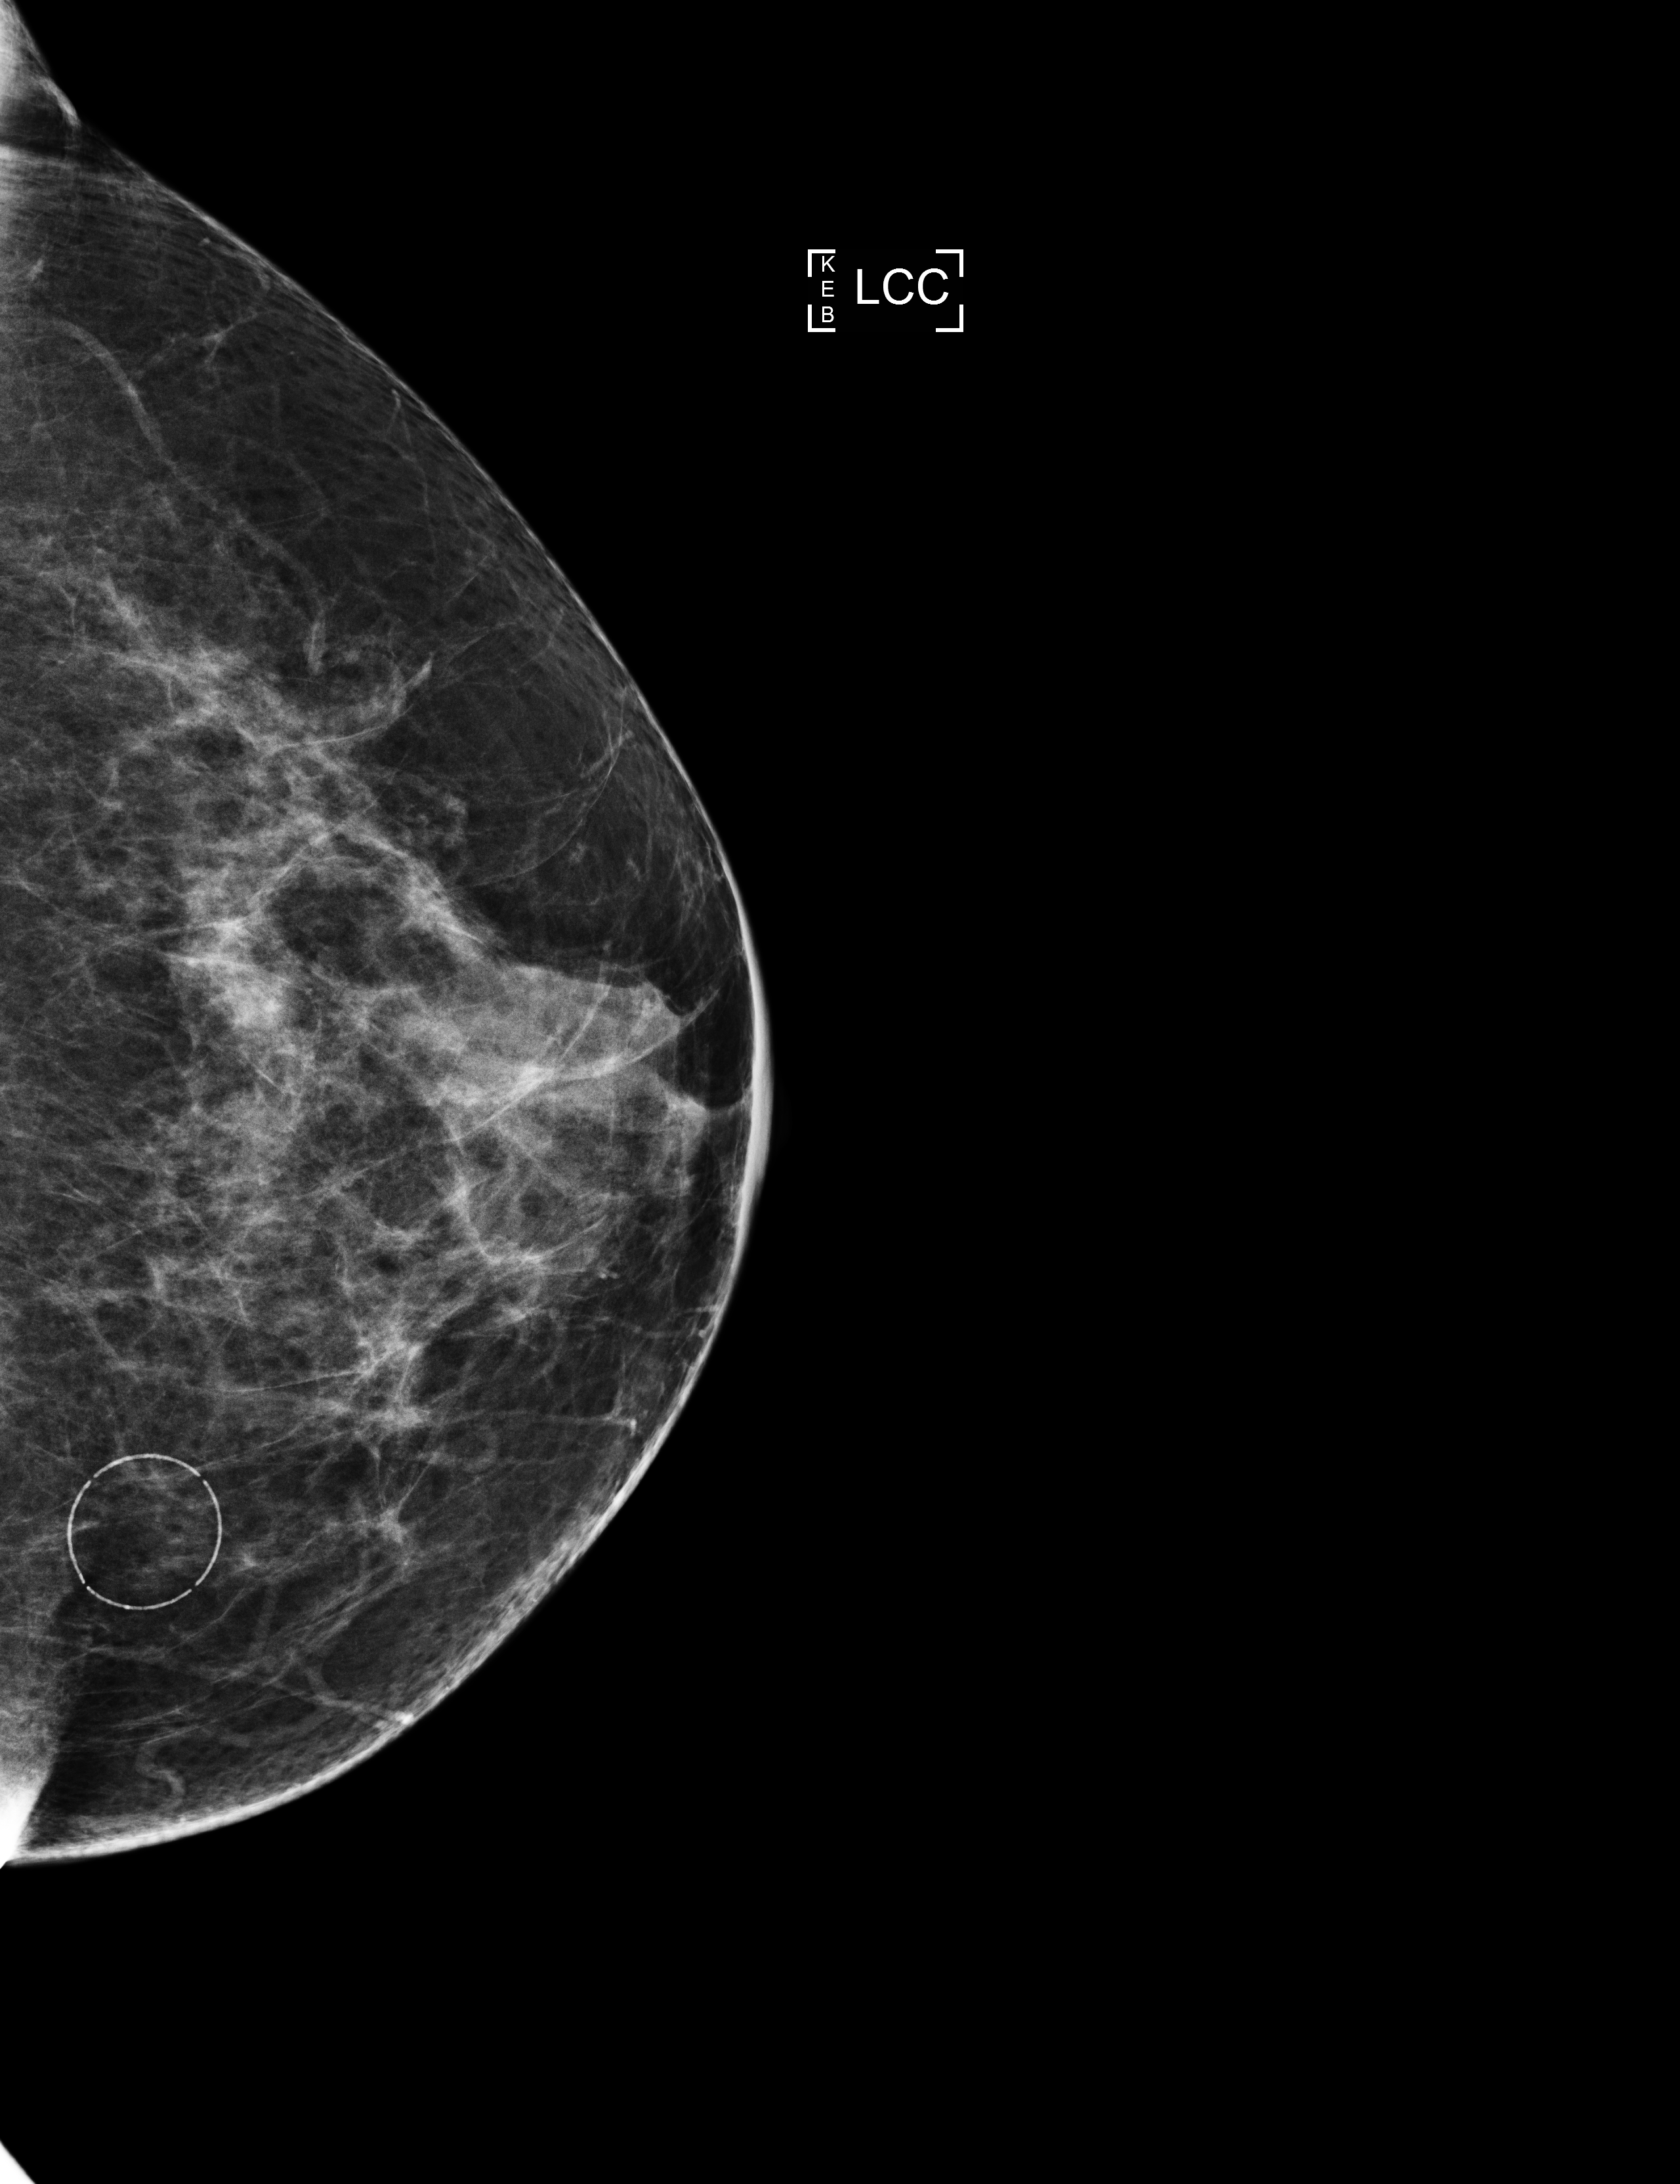
Digital mammogram (FFDM), left breast, cranio-caudal projection, screening examination. Female patient, age 60 years.
BI-RADS breast density category at the screening exam (both breasts, scale 1–4): 3. Final BI-RADS assessment for this screening round (tomosynthesis exam, both breasts): category 1. Recall: no recall after this screen.